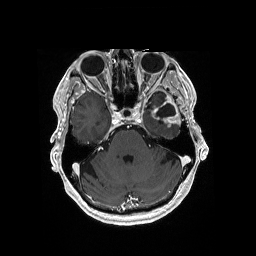
Brain MRI from a brain-tumour surgery series, one axial slice. Position 126 of 176 along the scan axis. T1-weighted post-contrast. 1 mm slice thickness. 256 × 256 image matrix, field of view 256 × 256 mm. Case-level facts recorded for this patient, not image findings: histopathology: Glioblastoma; WHO grade: 4; IDH mutation: no.
Structures marked on this image (outlined manually by an expert reader):
- previous resection cavity: bounding box <155,103,175,117> (left, top, right, bottom; pixels)
- tumour: <153,114,181,129>